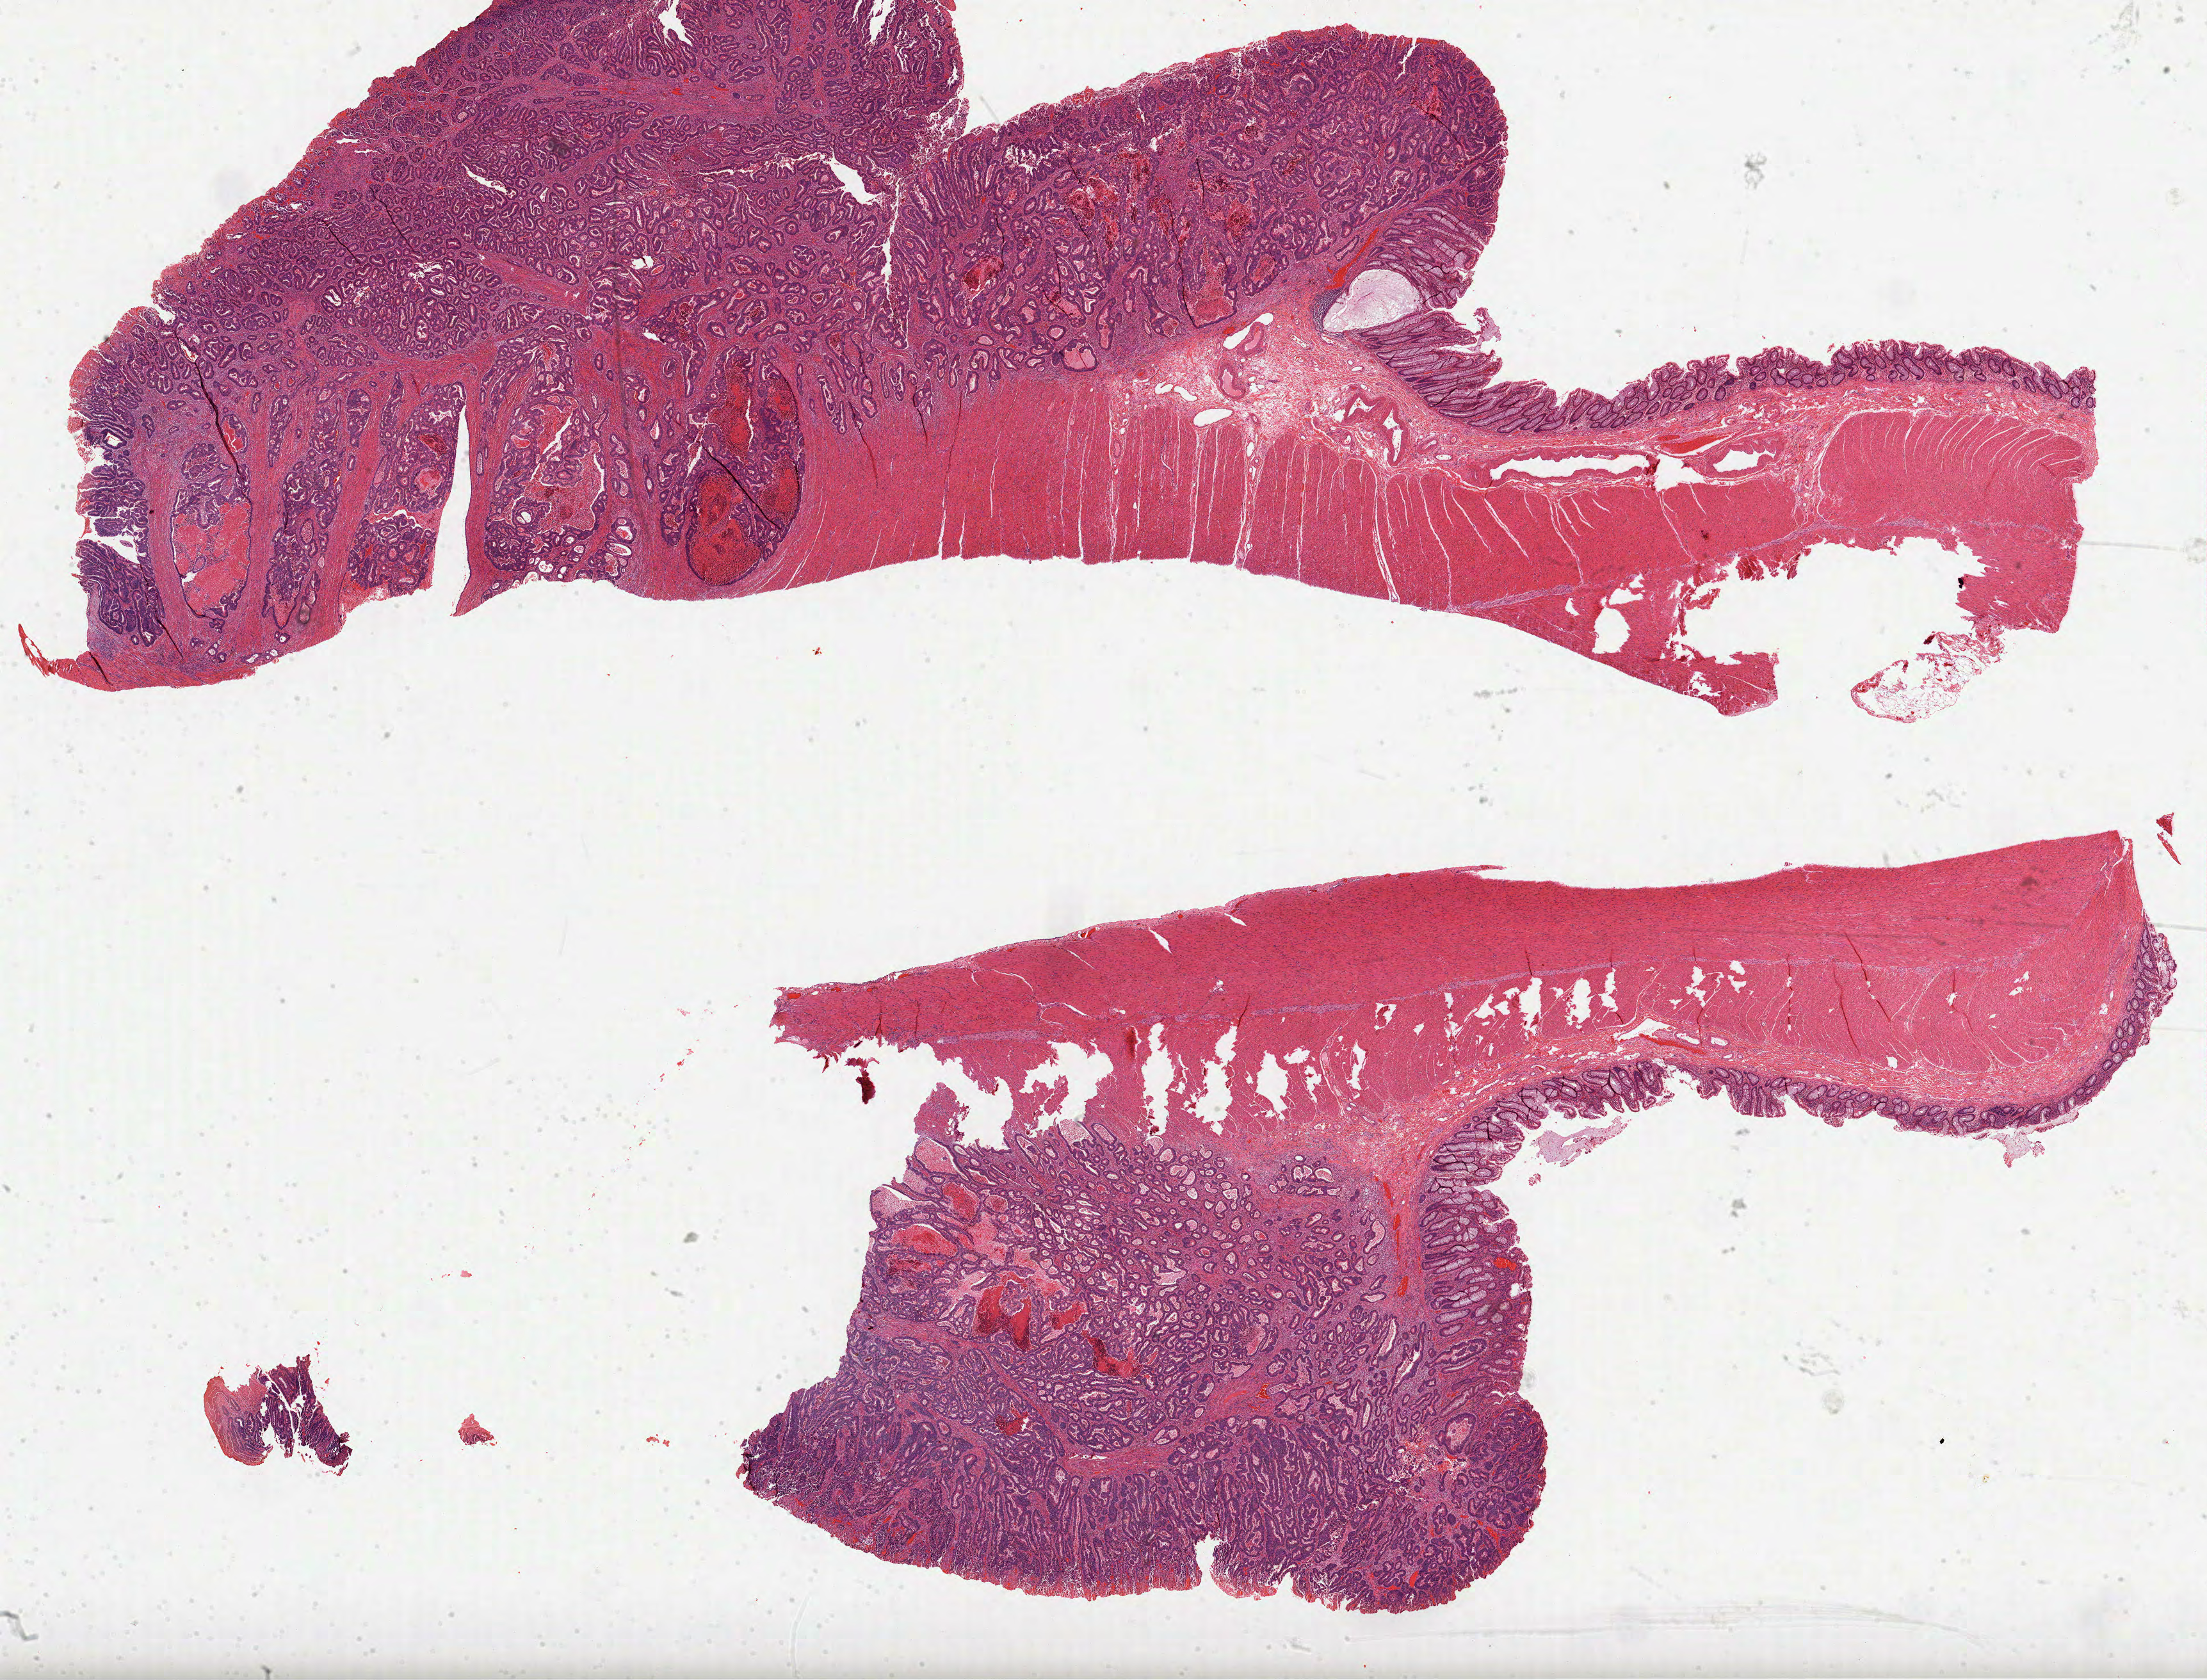
Hematoxylin and eosin (H&E) stained whole-slide image — whole scanned area (about 27.8 x 21.2 mm, from a 40x scan) shown as a low-resolution overview, FFPE section, colon, primary tumour sample. Female, age 77 years at initial diagnosis.
• lymph nodes positive (case pathology): 0 of 3 examined
• diagnosis: Adenocarcinoma, NOS (sigmoid colon)